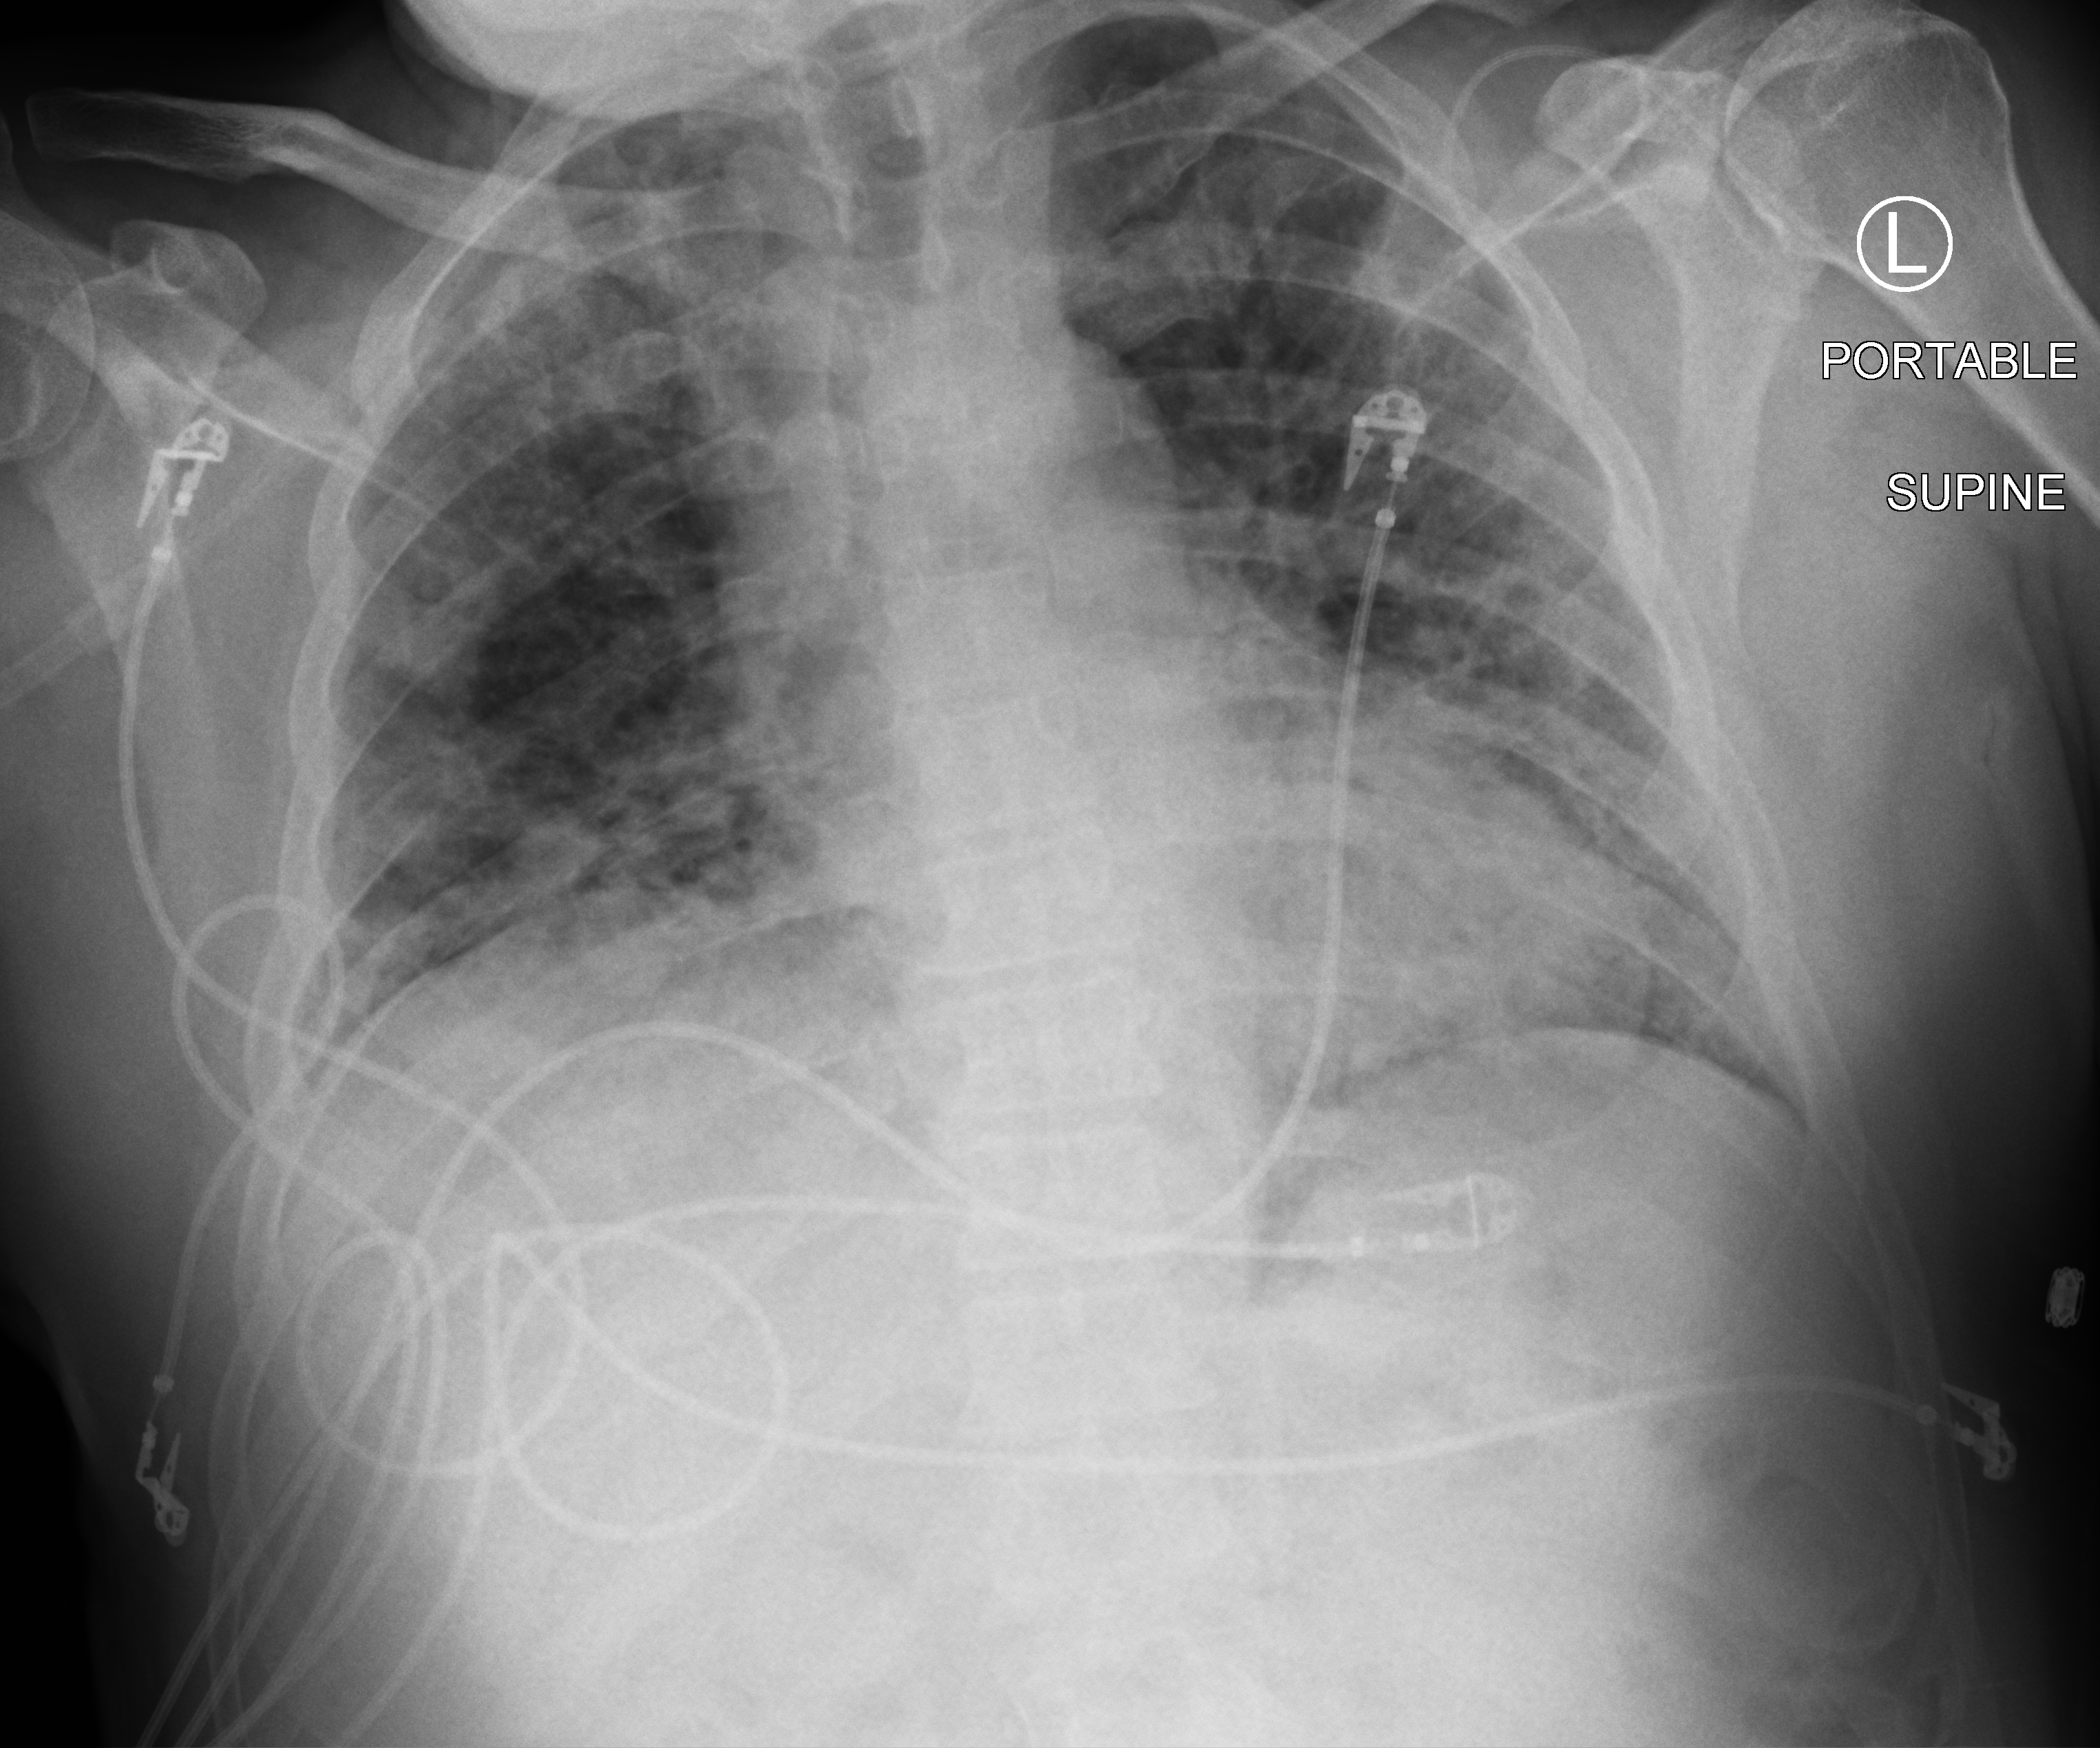
Bedside chest radiograph (computed radiography), anteroposterior (AP) projection. Patient hospitalised with COVID-19; male, aged 18–59 years.
Hospital-stay facts (about this admission, not read from this image; timing relative to this image not recorded):
- mechanically ventilated during this hospital stay: yes